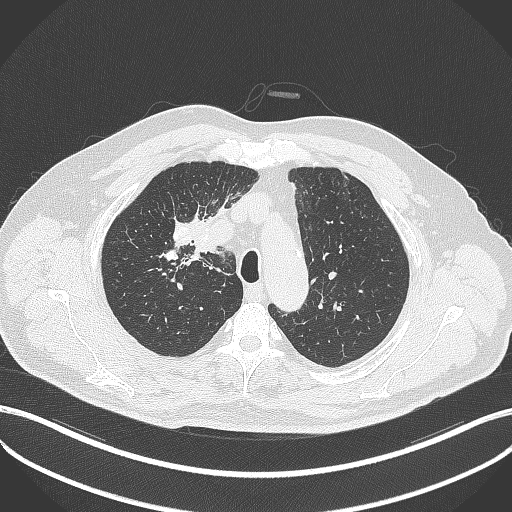
Chest CT, one axial slice. Slice 303 of 411 in the series (ordered by position). Lung window (W 1500 / L -600 HU). 512 × 512 image matrix, field of view 400 × 400 mm. Patient: male, 60 years. From the clinical record (not read from this slice): clinical TNM (as recorded): T1b N1 M0.
Structures marked on this image (bounding box drawn by a radiologist):
- lung tumour (recorded histology: squamous cell carcinoma): bounding box (x1, y1, x2, y2) in pixels: (189, 227, 219, 266)